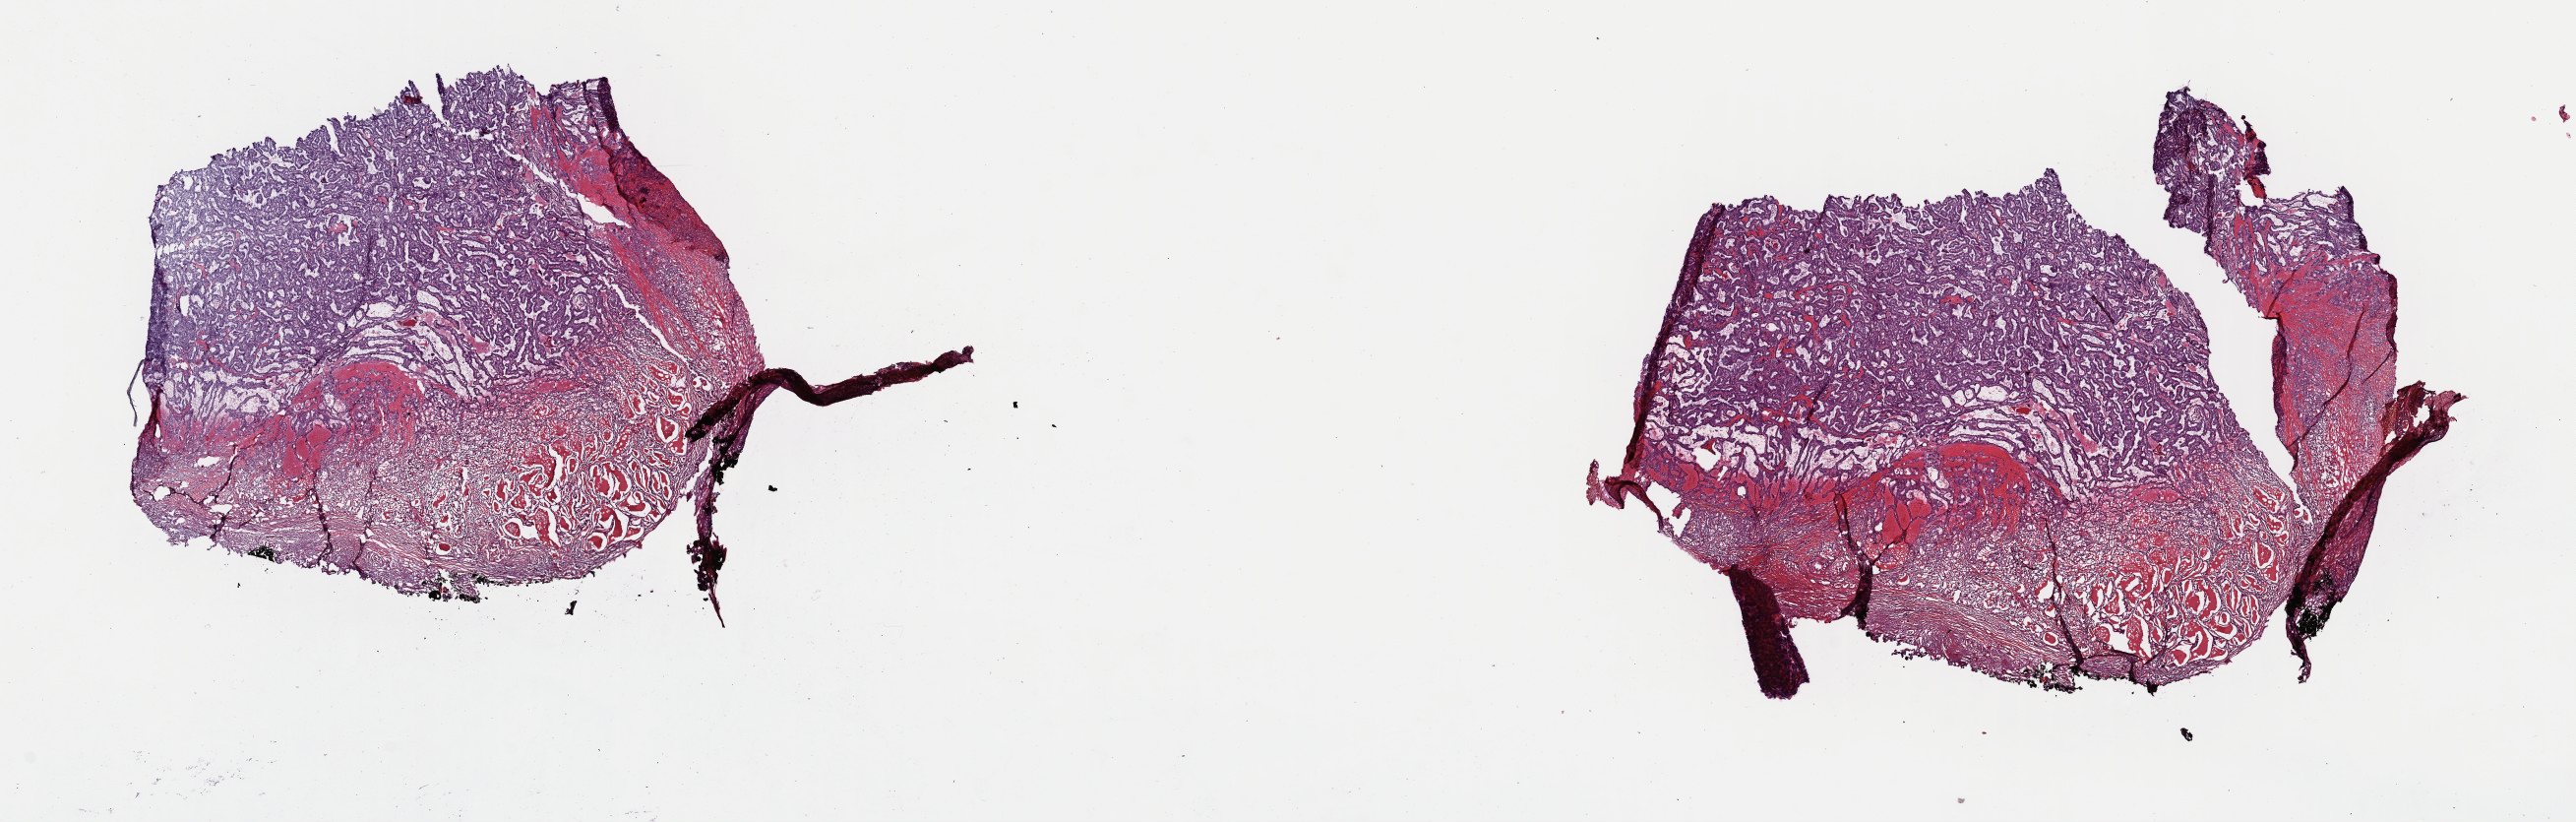
Hematoxylin and eosin (H&E) stained whole-slide image, whole scanned area (about 20.7 x 6.6 mm, from a 40x scan) shown as a low-resolution overview; frozen section from the top of the tissue portion; sample: primary tumour, thyroid. Female patient; age at initial diagnosis 68 years. Slide review estimates, as recorded: tumour cells 85%, tumour nuclei 100%, normal cells 0%, stromal cells 15%, necrosis 0%. Infiltration values recorded for this section: lymphocyte infiltration 1%, monocyte infiltration 0%, neutrophil infiltration 0%.
AJCC pathologic stage: I. Lymph nodes positive (case pathology): 0 of 3 examined. Histologic diagnosis: Papillary adenocarcinoma, NOS. TNM: T1b N0 M0. Laterality: left.